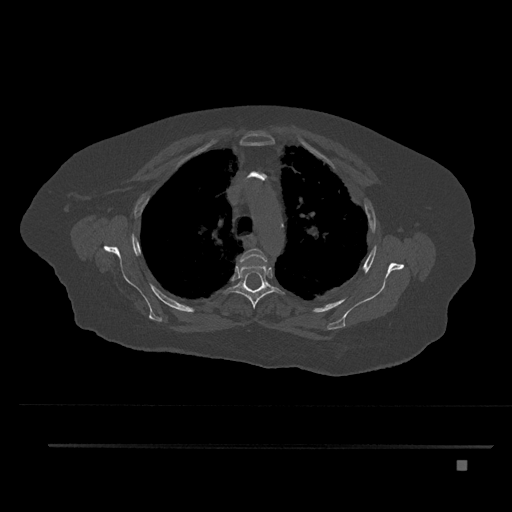
CT including the spine, one axial slice. Position 607 of 797 along the scan axis. Reconstruction kernel Br40s/3. Bone window (W 1800 / L 400 HU). 512 × 512 image matrix, field of view 437 × 437 mm. Female patient, age 76 years. Case-level facts recorded for this patient, not image findings: primary cancer: lung.
Structures marked on this image (semi-automatic segmentation, software-assisted and operator-edited):
- T3 vertebra: bounding box (x1, y1, x2, y2) in pixels: (240, 248, 267, 265)
- T4 vertebra: (226, 257, 284, 309)